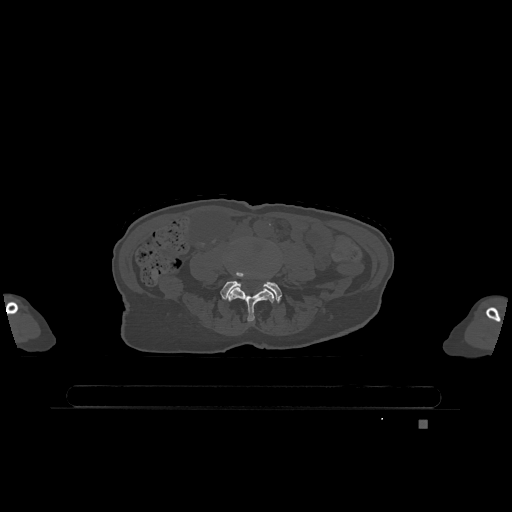
CT including the spine, one axial slice. Position 271 of 1317 along the scan axis. Bone window (W 1800 / L 400 HU). 0.5 mm slice thickness. 512 × 512 image matrix. Female patient, age 74 years. Case-level facts recorded for this patient, not image findings: primary cancer: lung; vertebrae with lytic lesions (as recorded): T1, T4, T5, T6, L4, L5.
Outlined on this slice (semi-automatically segmented with operator editing):
- L4 vertebra: bounding box <228,288,274,323> (left, top, right, bottom; pixels)
- L5 vertebra: <220,273,282,302>